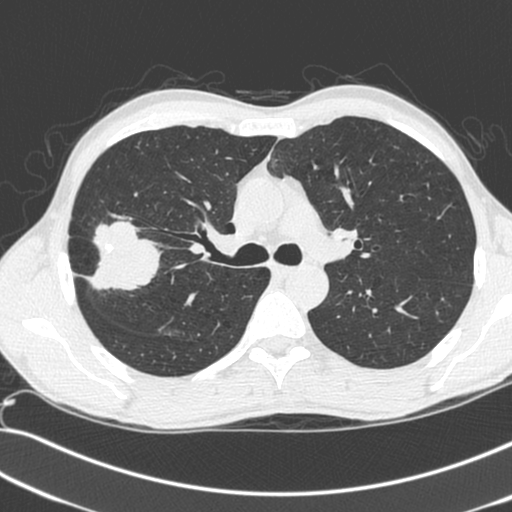
Axial slice from a low-dose chest CT screening exam. Baseline annual screen. Lung window (W 1500 / L -600 HU). Standard (soft-tissue) reconstruction kernel (C). Slice 87 of 281 in the series. Male participant, aged 55 years at enrolment. Current smoker at enrolment.
- Lesion marked by an expert reader, box from (x=68, y=223) to (x=155, y=299) px.
- Reader record for this screening exam (exam-level; its link to the box is not recorded): non-calcified nodule or mass ≥4 mm, right upper lobe, 52 × 39 mm, spiculated (stellate) margins, soft tissue attenuation.
- Official screen result: positive, change unspecified: nodule(s) >= 4 mm or enlarging nodule(s), mass(es), or other non-specific abnormalities suspicious for lung cancer.